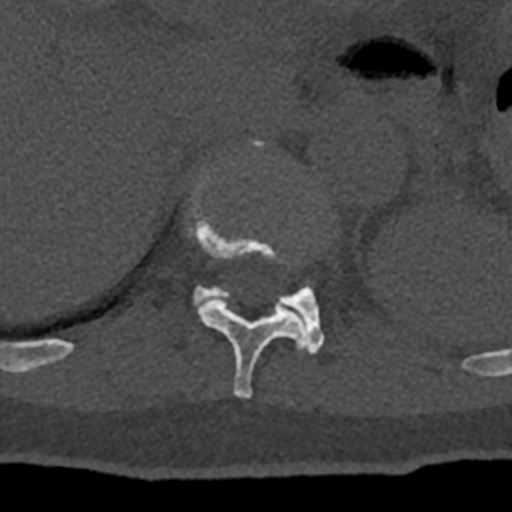
CT including the spine, one axial slice; position 528 of 797 along the scan axis; reconstruction kernel Br40s/3; bone window (W 1800 / L 400 HU); 512 × 512 image matrix. Patient: male, 74 years. Case-level facts recorded for this patient, not image findings: primary cancer: renal; vertebrae with lytic lesions (as recorded): T10, L1, L2, L3, L4, L5.
Outlined on this slice (semi-automatically segmented with operator editing):
- T11 vertebra: bounding box (x1, y1, x2, y2) in pixels: (71, 141, 307, 398)
- T12 vertebra: (193, 252, 324, 354)